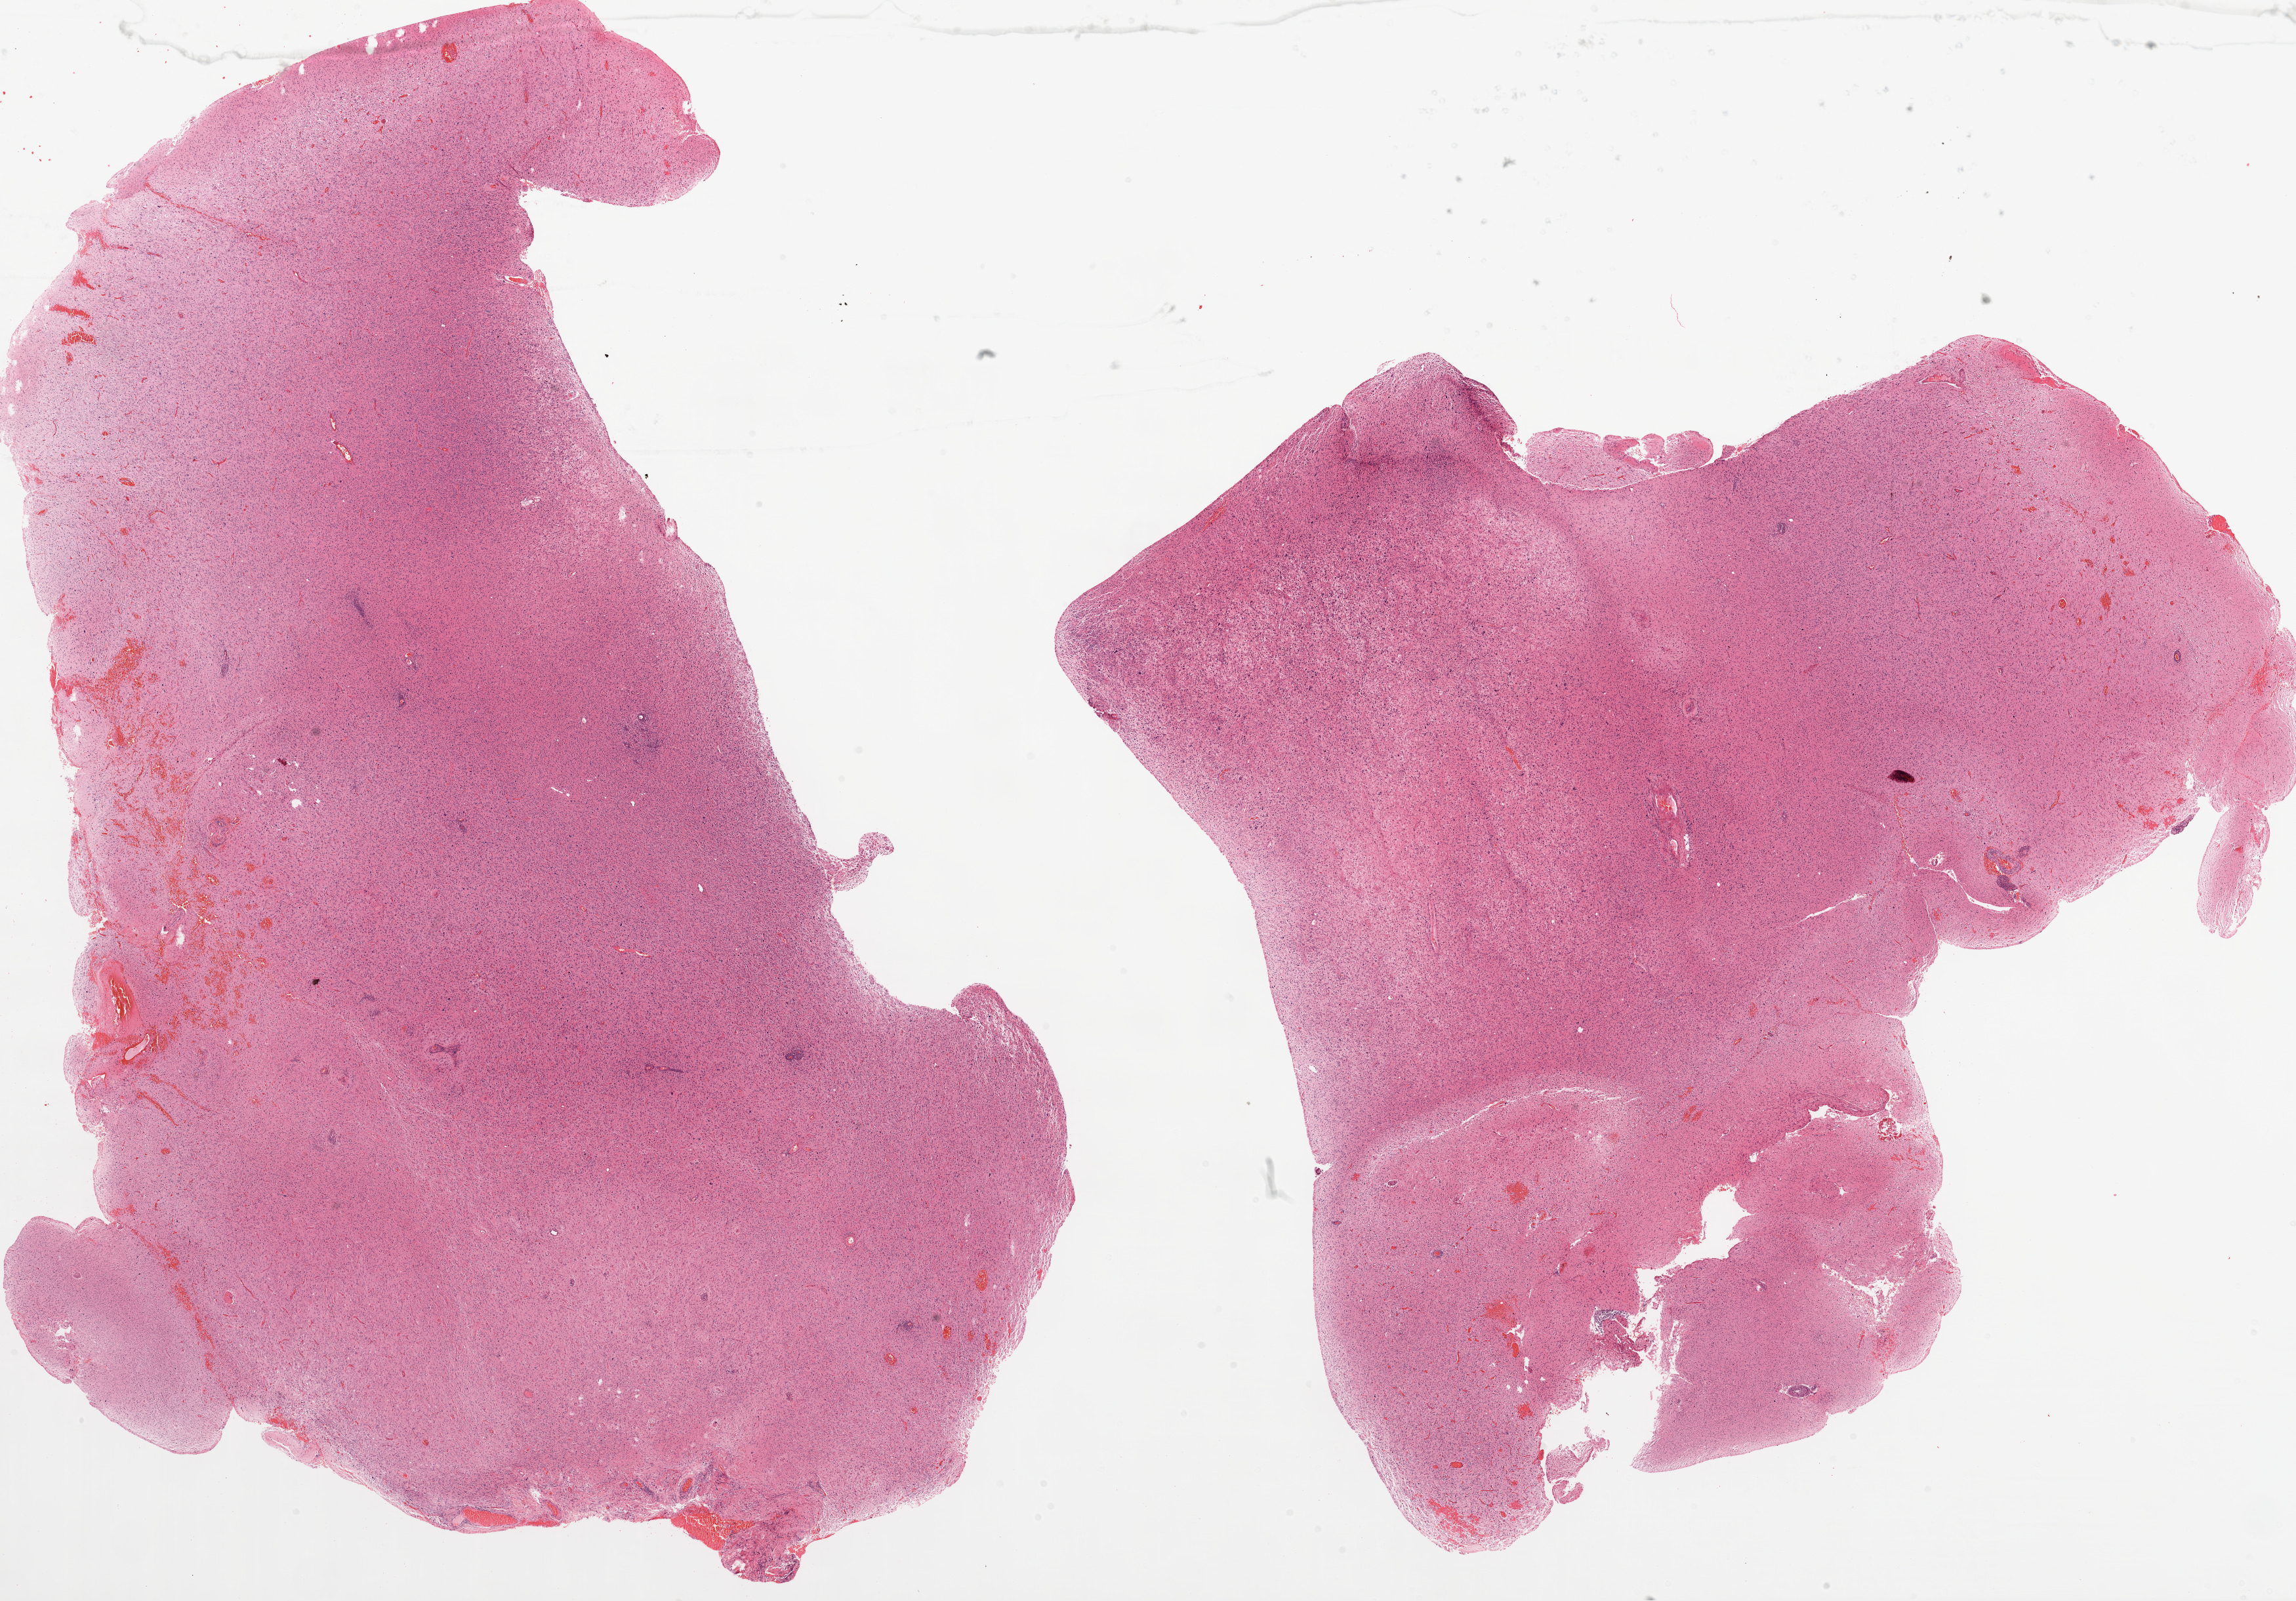
Whole-slide histology image, Hematoxylin and eosin (H&E) stained, whole scanned area (about 28.1 x 19.6 mm, from a 20x scan) shown as a low-resolution overview. Formalin-fixed paraffin-embedded (FFPE) diagnostic section. Sample: primary tumour, brain. Patient: female, age at initial diagnosis 20 years.
* histologic diagnosis: Glioblastoma